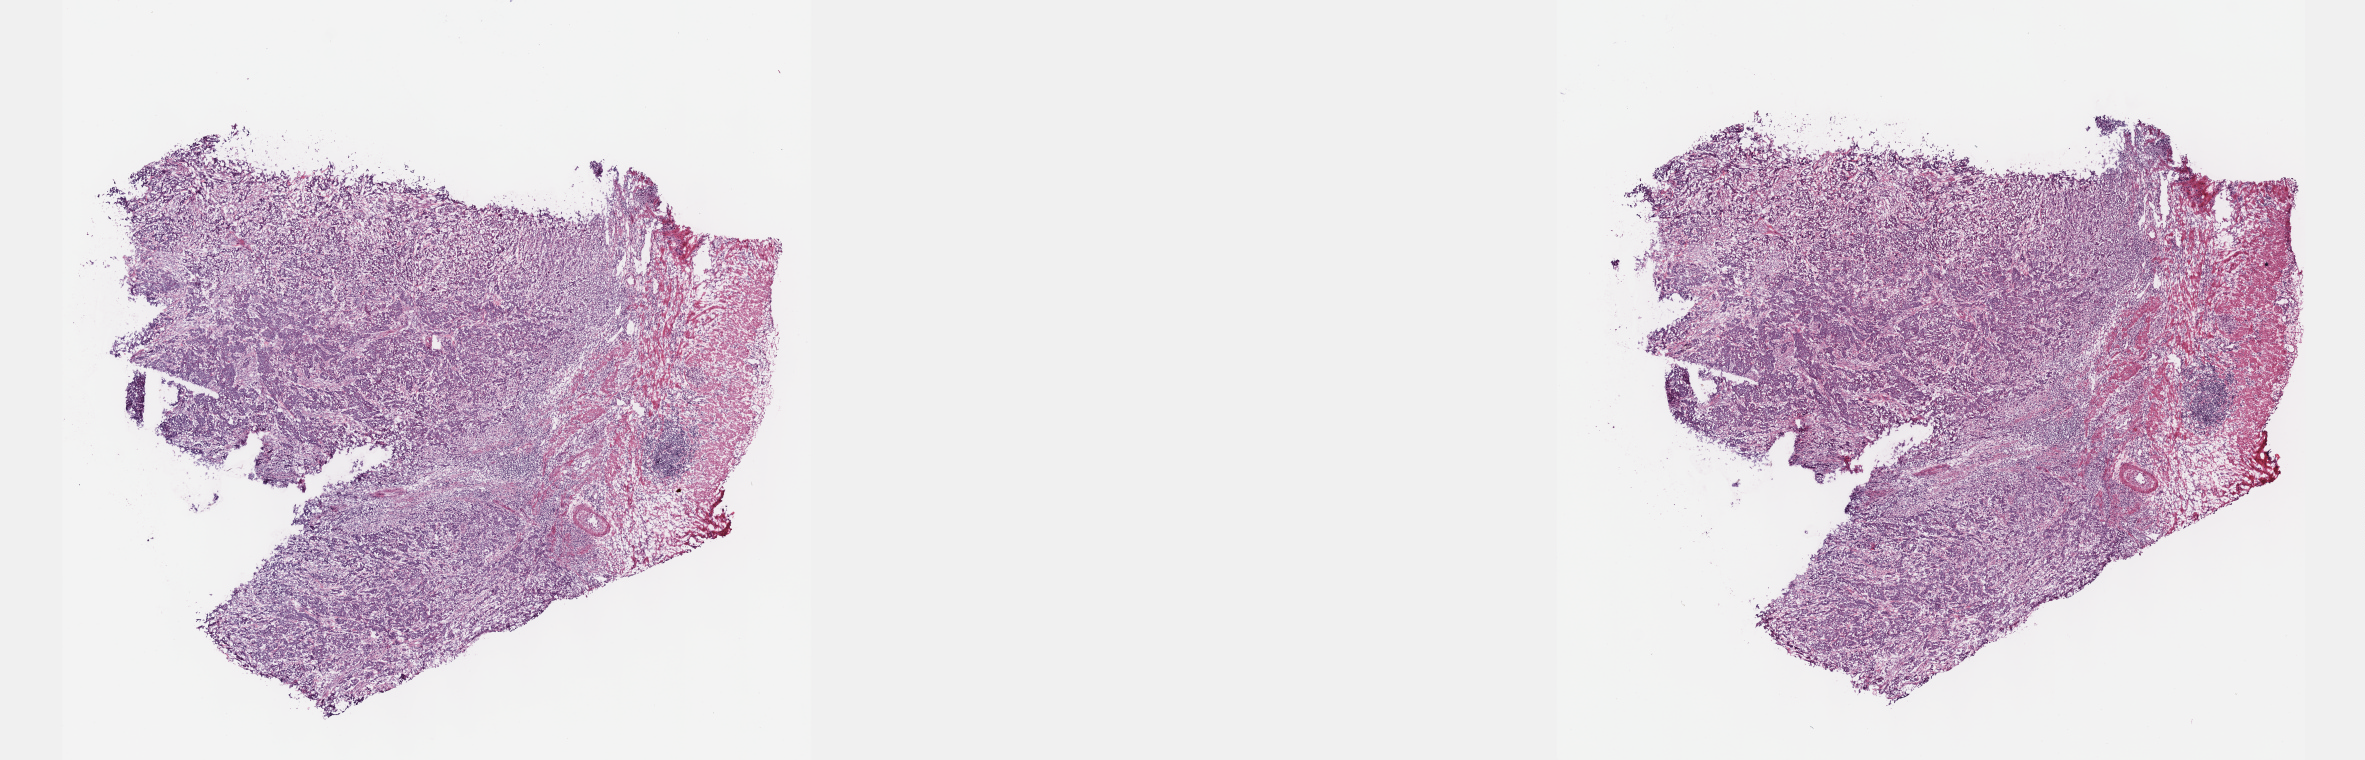
Hematoxylin and eosin (H&E) stained whole-slide image, shown as a low-resolution overview of the whole scanned area (about 19.1 x 6.1 mm, acquisition: 40x scan); frozen section from the top of the tissue portion; primary tumour sample from the stomach. Female, age 61 years at initial diagnosis. Histologic grade: GX (grade cannot be assessed). Pathologist review of this section (percent, as recorded): tumour cells 80%, tumour nuclei 80%, normal cells 0%, stromal cells 10%, necrosis 10%. Inflammatory infiltration, as recorded: lymphocyte infiltration 40%, monocyte infiltration 20%, neutrophil infiltration 20%.
Pathologic diagnosis: Signet ring cell carcinoma (gastric antrum). AJCC pathologic stage: IB (7th edition).